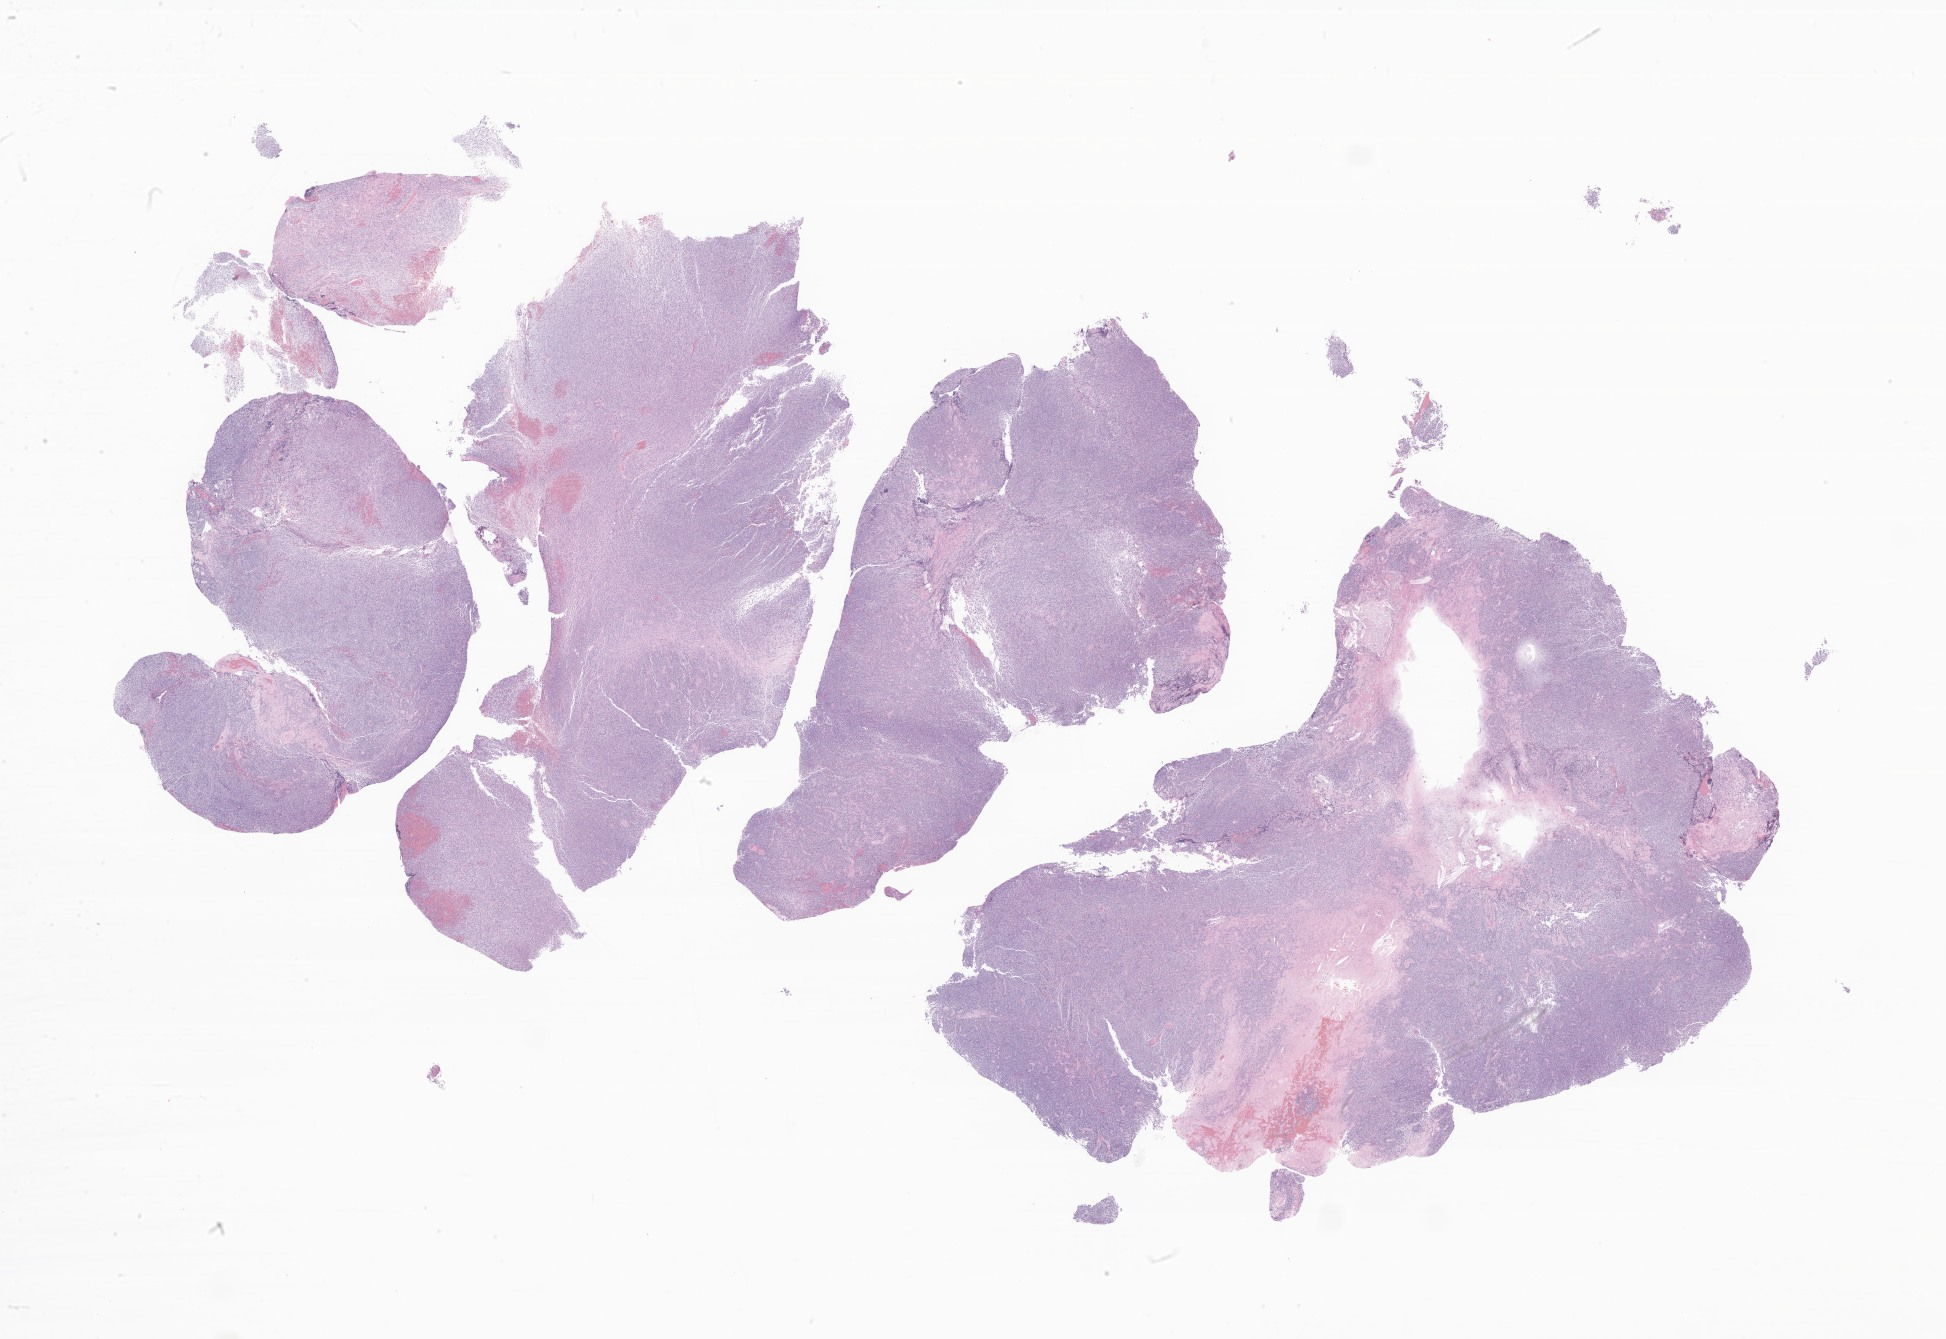
Hematoxylin and eosin (H&E) whole-slide image of tumor tissue from the brain, whole scanned area (about 32.8 x 22.6 mm) shown as a low-resolution overview. Formalin-fixed paraffin-embedded section. Patient: male, age 106 months (8 years 10 months).
Diagnosis: Medulloblastoma, NOS.